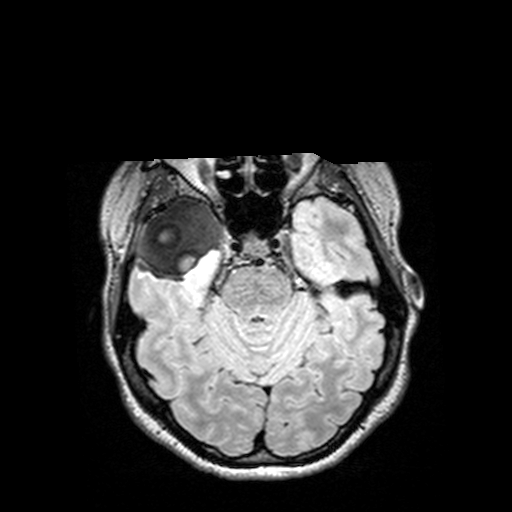
Brain MRI from a brain-tumour surgery series, one axial slice; T2 FLAIR; 1 mm slice thickness; 512 × 512 image matrix. Case-level facts recorded for this patient, not image findings: histopathology: Astrocytoma; WHO grade: 3.
Outlined on this slice (outlined manually by an expert reader):
- tumour: bounding box (x1, y1, x2, y2) in pixels: (126, 197, 232, 282)